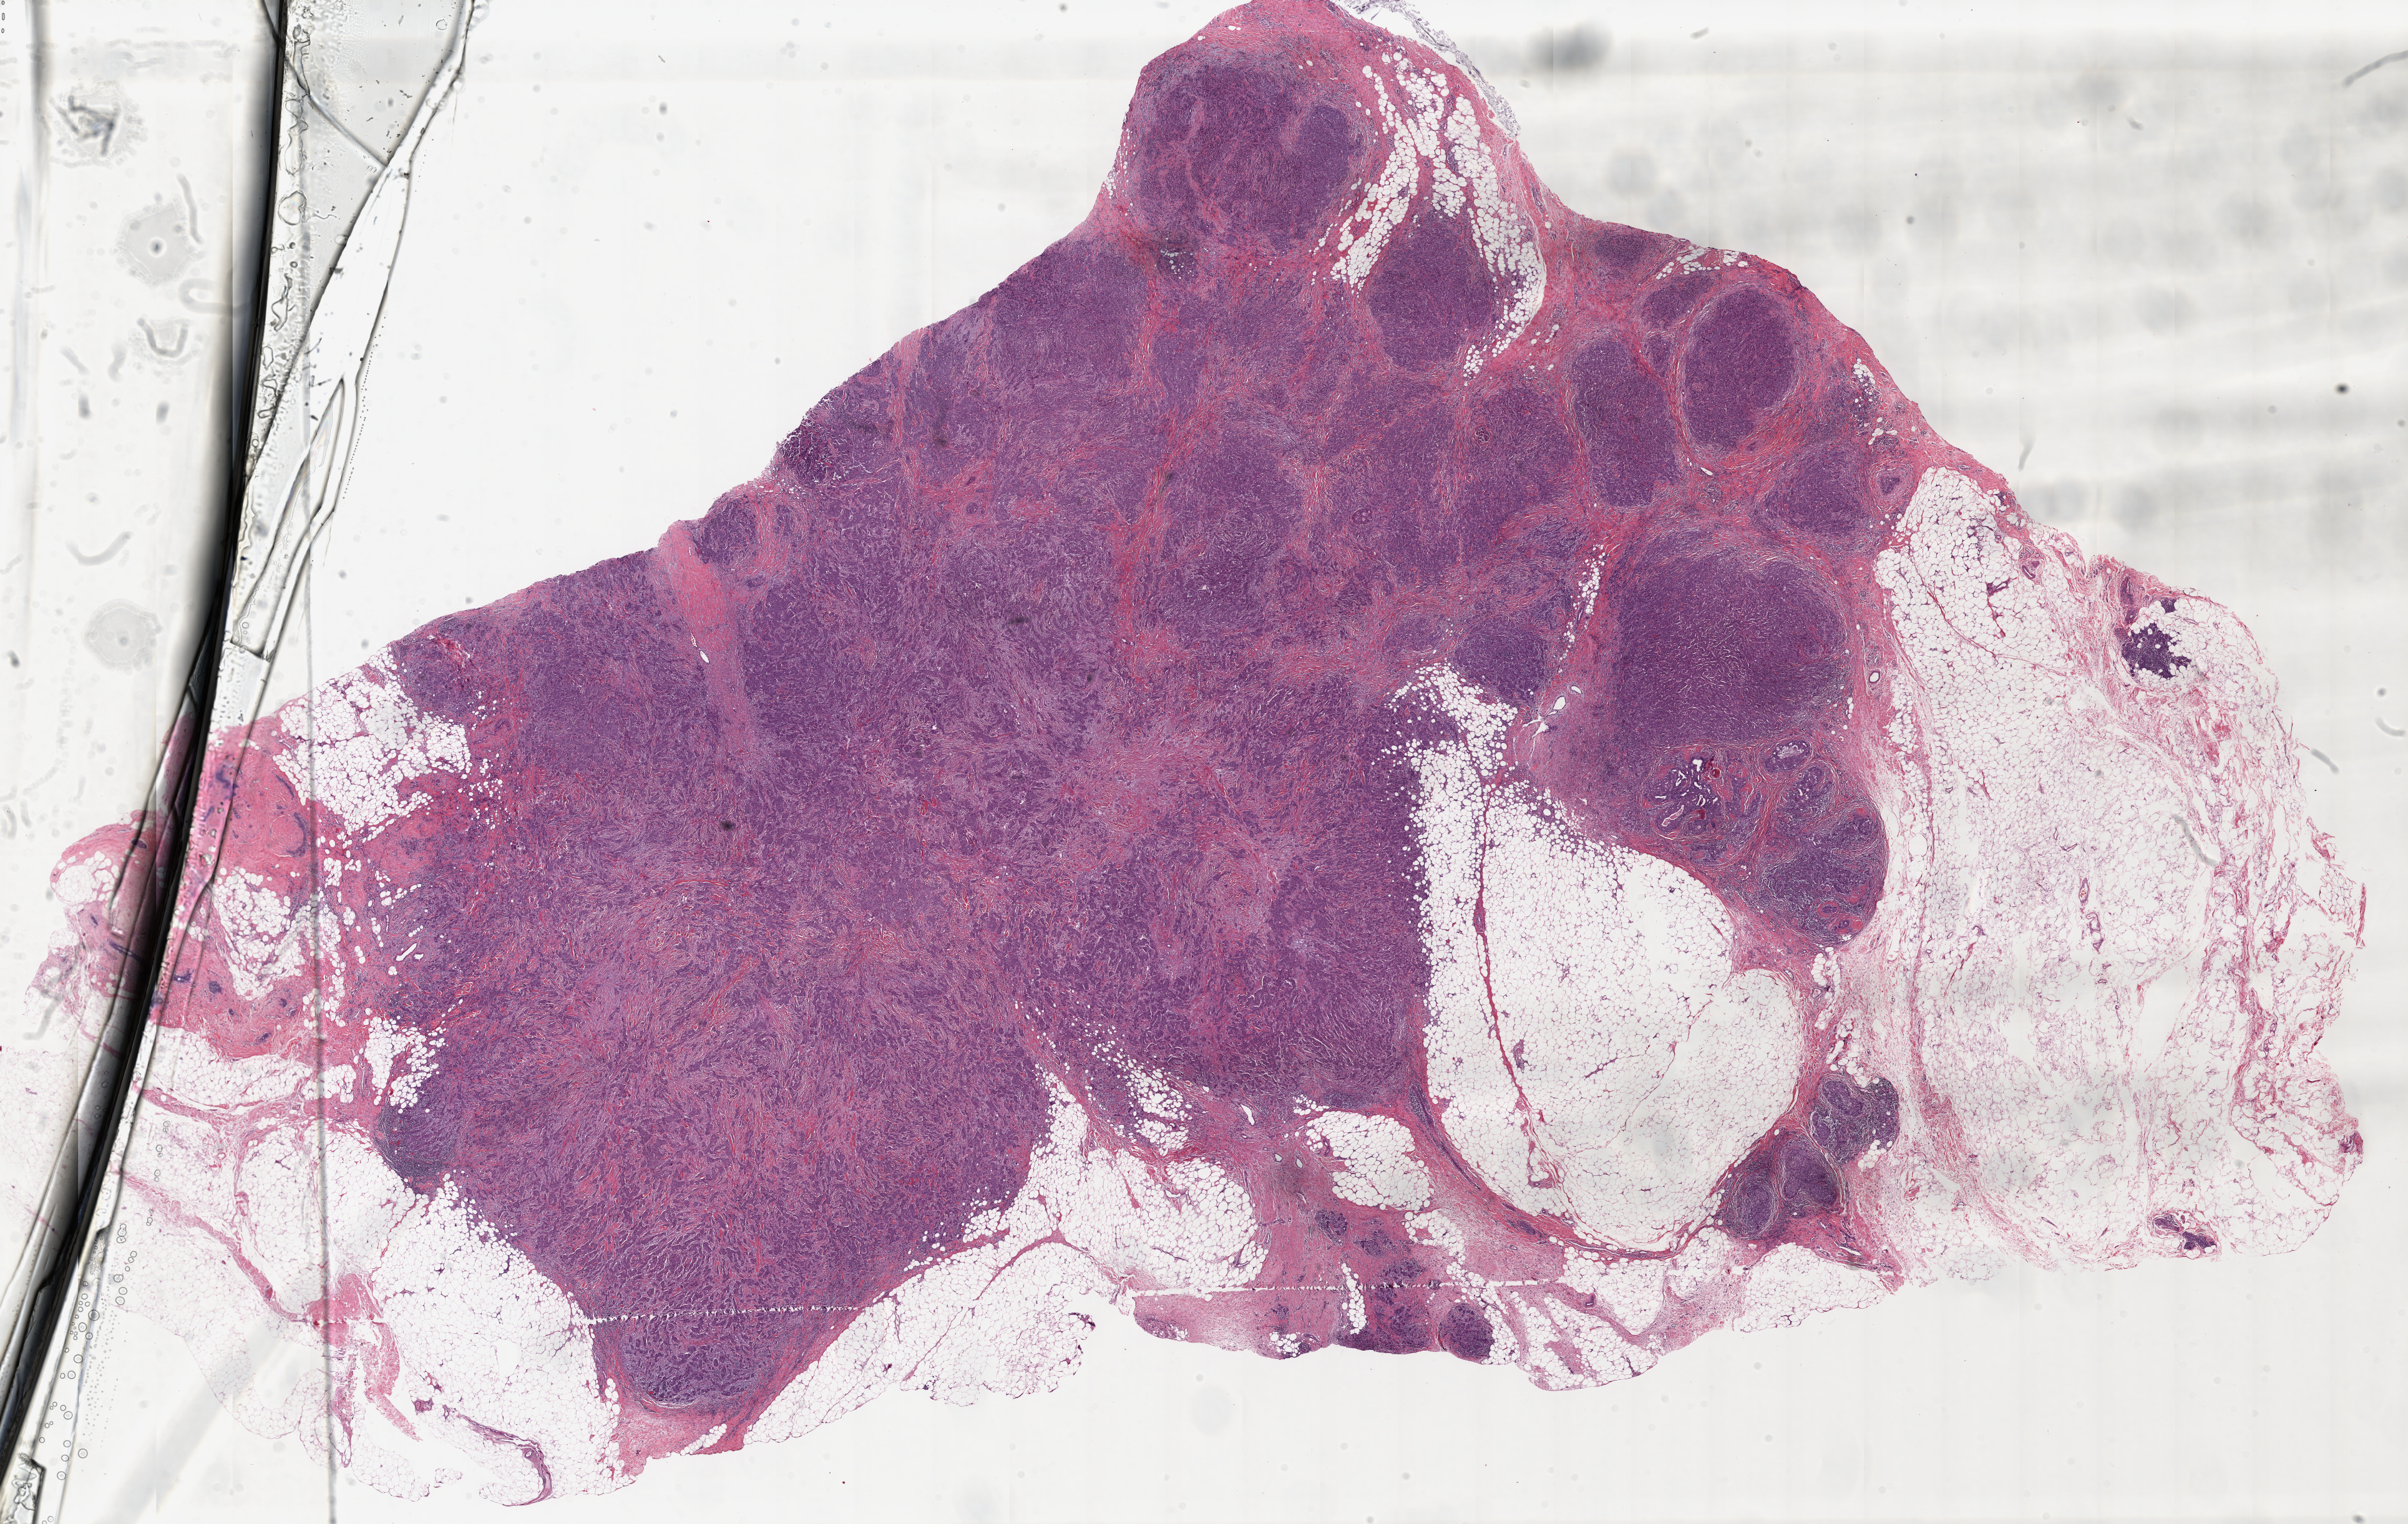
Whole-slide histology image, H&E, a low-resolution overview of the entire scanned area, about 30.8 x 19.5 mm. Formalin-fixed paraffin-embedded (FFPE) diagnostic section. Primary tumour sample from the breast. Female patient; age at initial diagnosis 53 years.
- AJCC pathologic stage: IIIA
- lymph nodes positive (case pathology): 8 of 29 examined
- TNM: T2 N2a M0
- histologic diagnosis: Infiltrating duct carcinoma, NOS